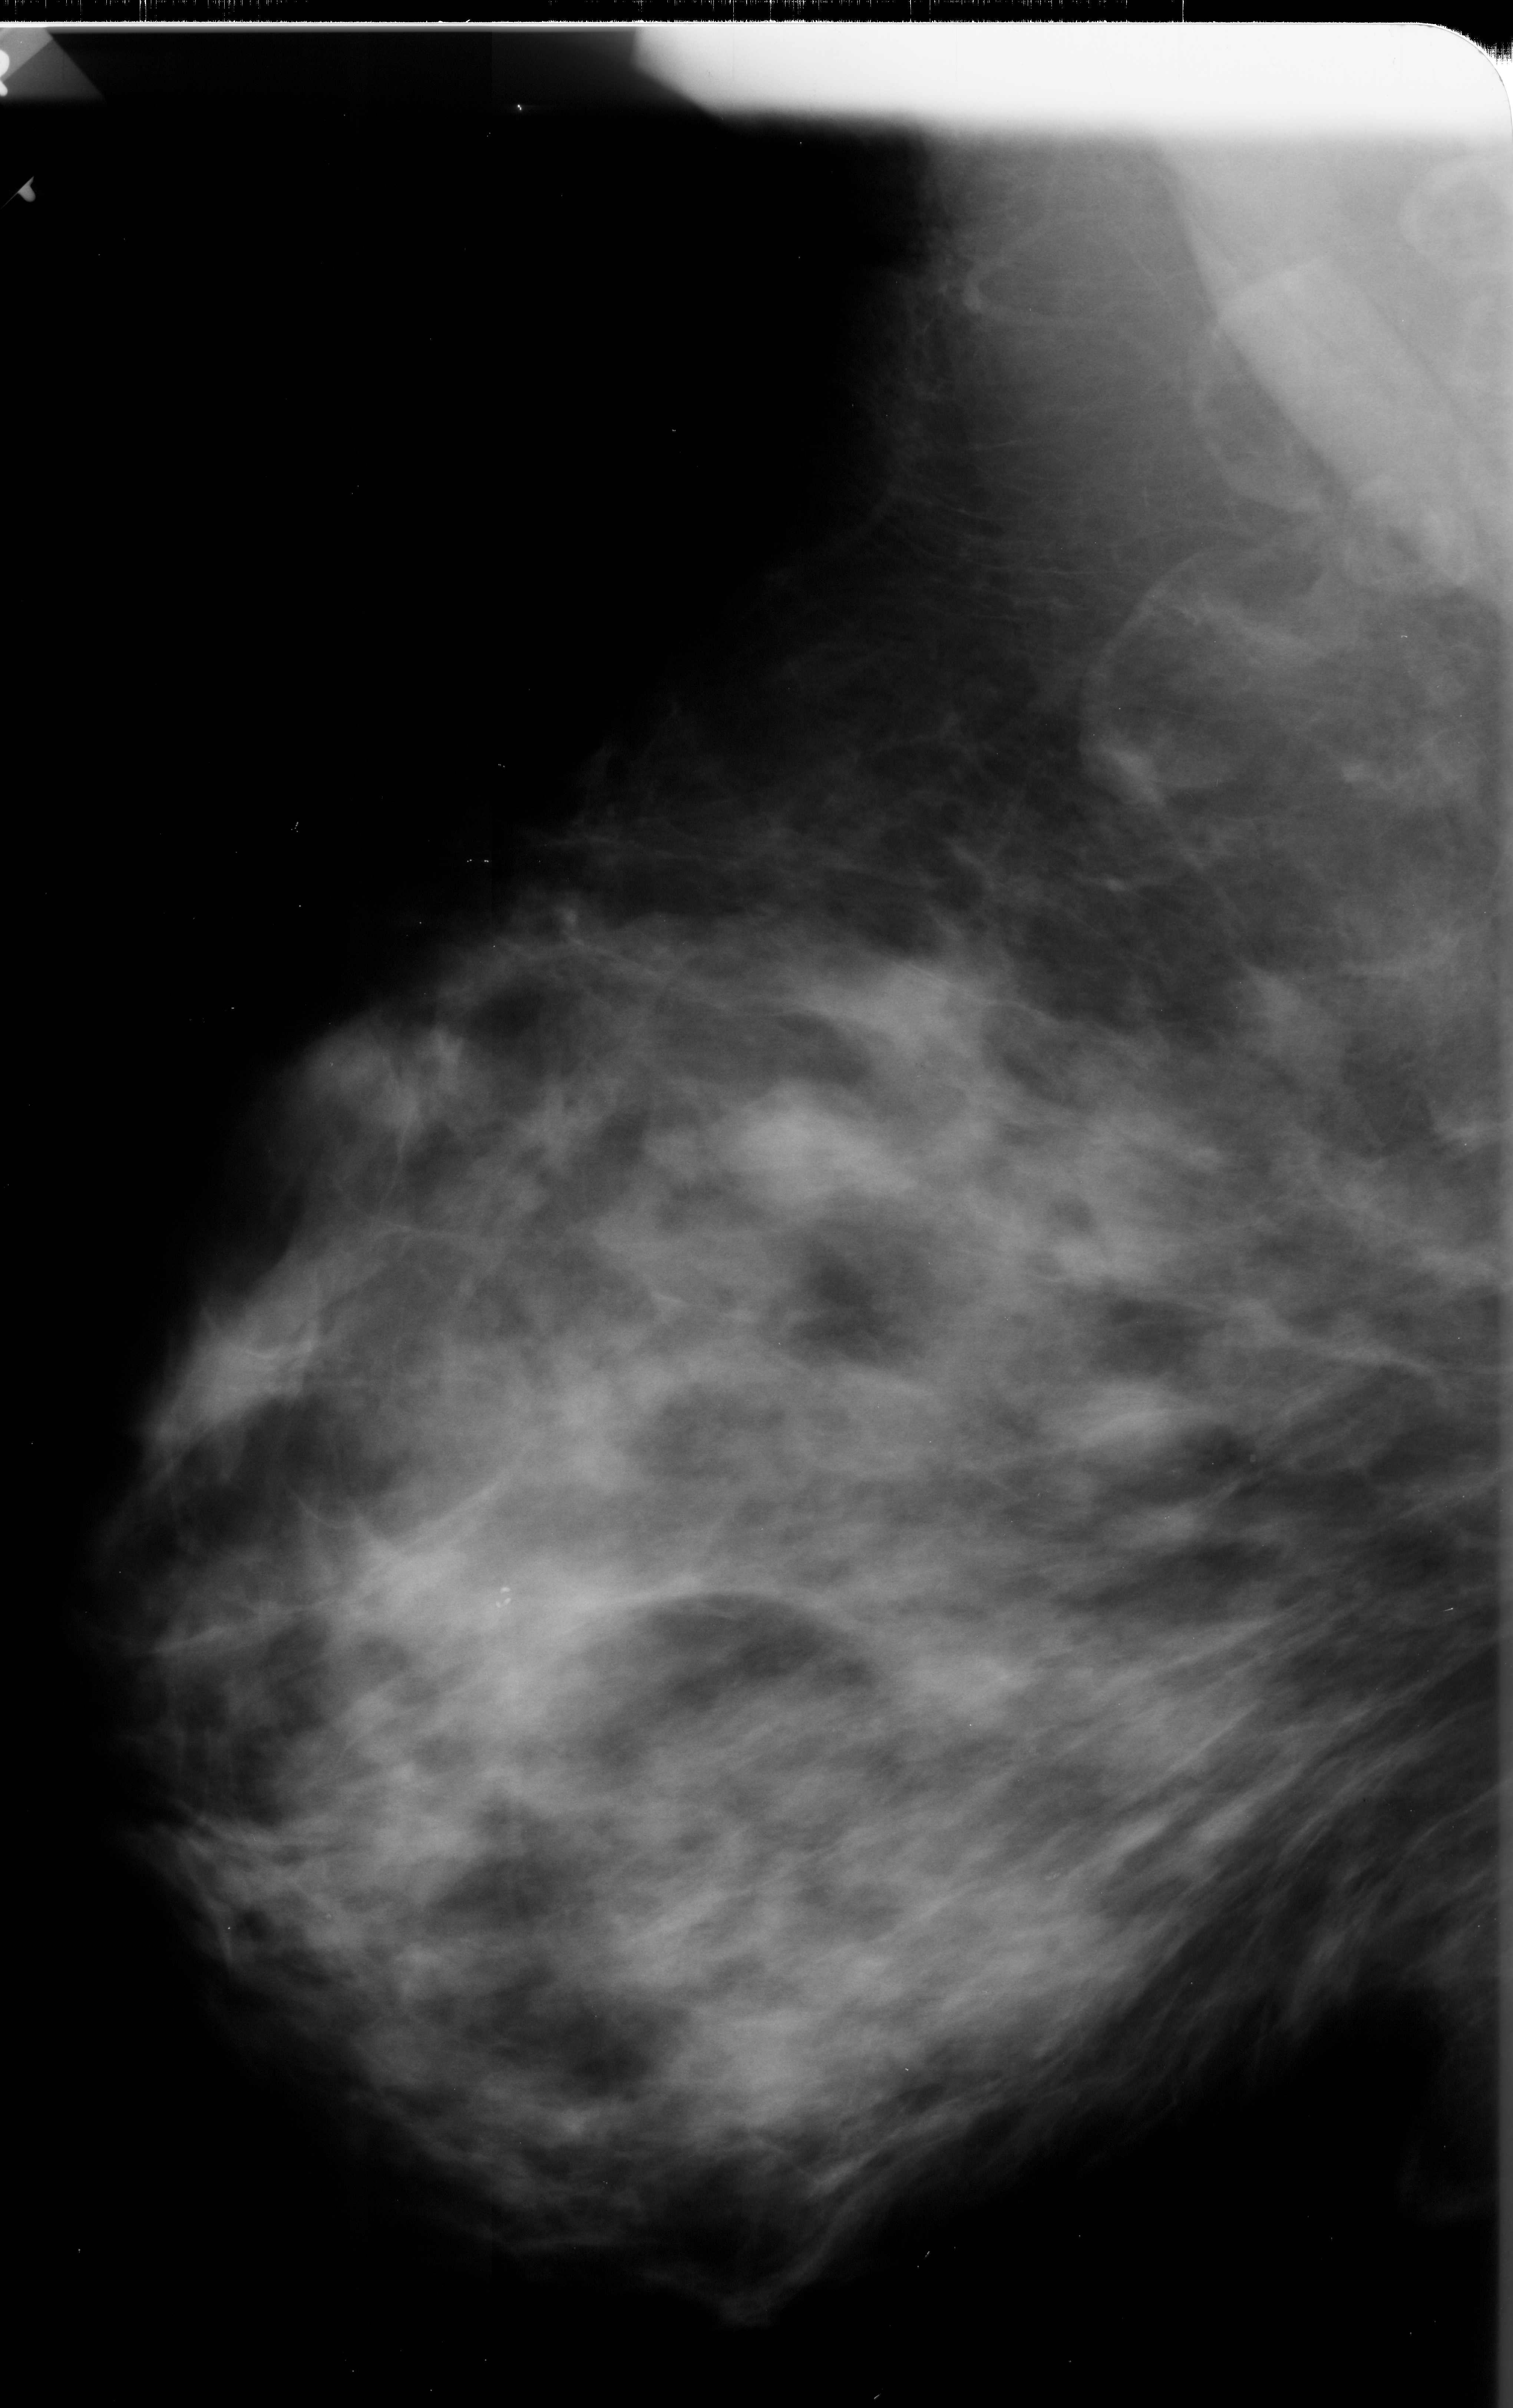
Scanned film-screen mammogram; left breast; mediolateral oblique (MLO) view; BI-RADS breast density category 4 (scale 1–4); 1513 × 2408 image matrix.
Expert-marked regions of interest on this film, with their recorded descriptors:
- calcifications, morphology pleomorphic, distribution linear; BI-RADS assessment category 4; pathology (as recorded): malignant: bounding box <1020,1854,1086,1892> (left, top, right, bottom; pixels)